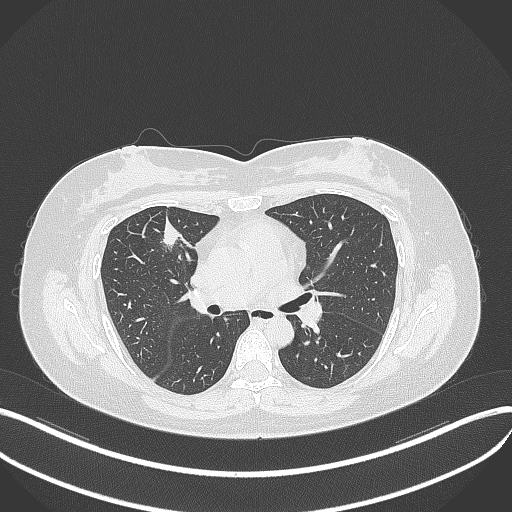
Chest CT, one axial slice. Position 182 of 273 along the scan axis. Reconstruction kernel B70f. Lung window (W 1500 / L -600 HU). 1 mm slice thickness. 512 × 512 image matrix, field of view 400 × 400 mm. Female patient, age 42 years. From the clinical record (not read from this slice): clinical TNM (as recorded): T1b N0 M0.
Annotated regions visible in this slice (bounding box drawn by a radiologist):
- lung tumour (recorded histology: adenocarcinoma): bounding box <155,217,187,253> (left, top, right, bottom; pixels)